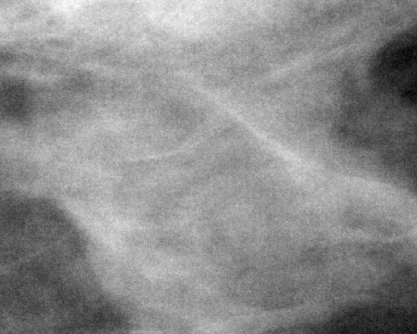
Cropped region of a digitized screen-film mammogram centred on a radiologist-marked abnormality; right breast; CC view.
Mass, shape lobulated, margins obscured; BI-RADS assessment category 3; subtlety rating 4 on a 1 (subtle) to 5 (obvious) scale; benign without callback (not worked up further).